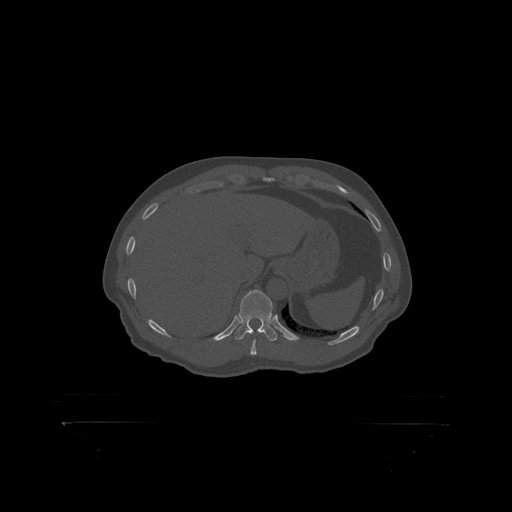
CT including the spine, one axial slice; position 384 of 399 along the scan axis; reconstruction kernel STANDARD; 120 kVp; bone window (W 1800 / L 400 HU); 512 × 512 image matrix, field of view 650 × 650 mm. Patient: male, 46 years. Case-level facts recorded for this patient, not image findings: primary cancer: skin.
Structures marked on this image (semi-automatically segmented with operator editing):
- T11 vertebra: bounding box (x1, y1, x2, y2) in pixels: (239, 290, 273, 319)